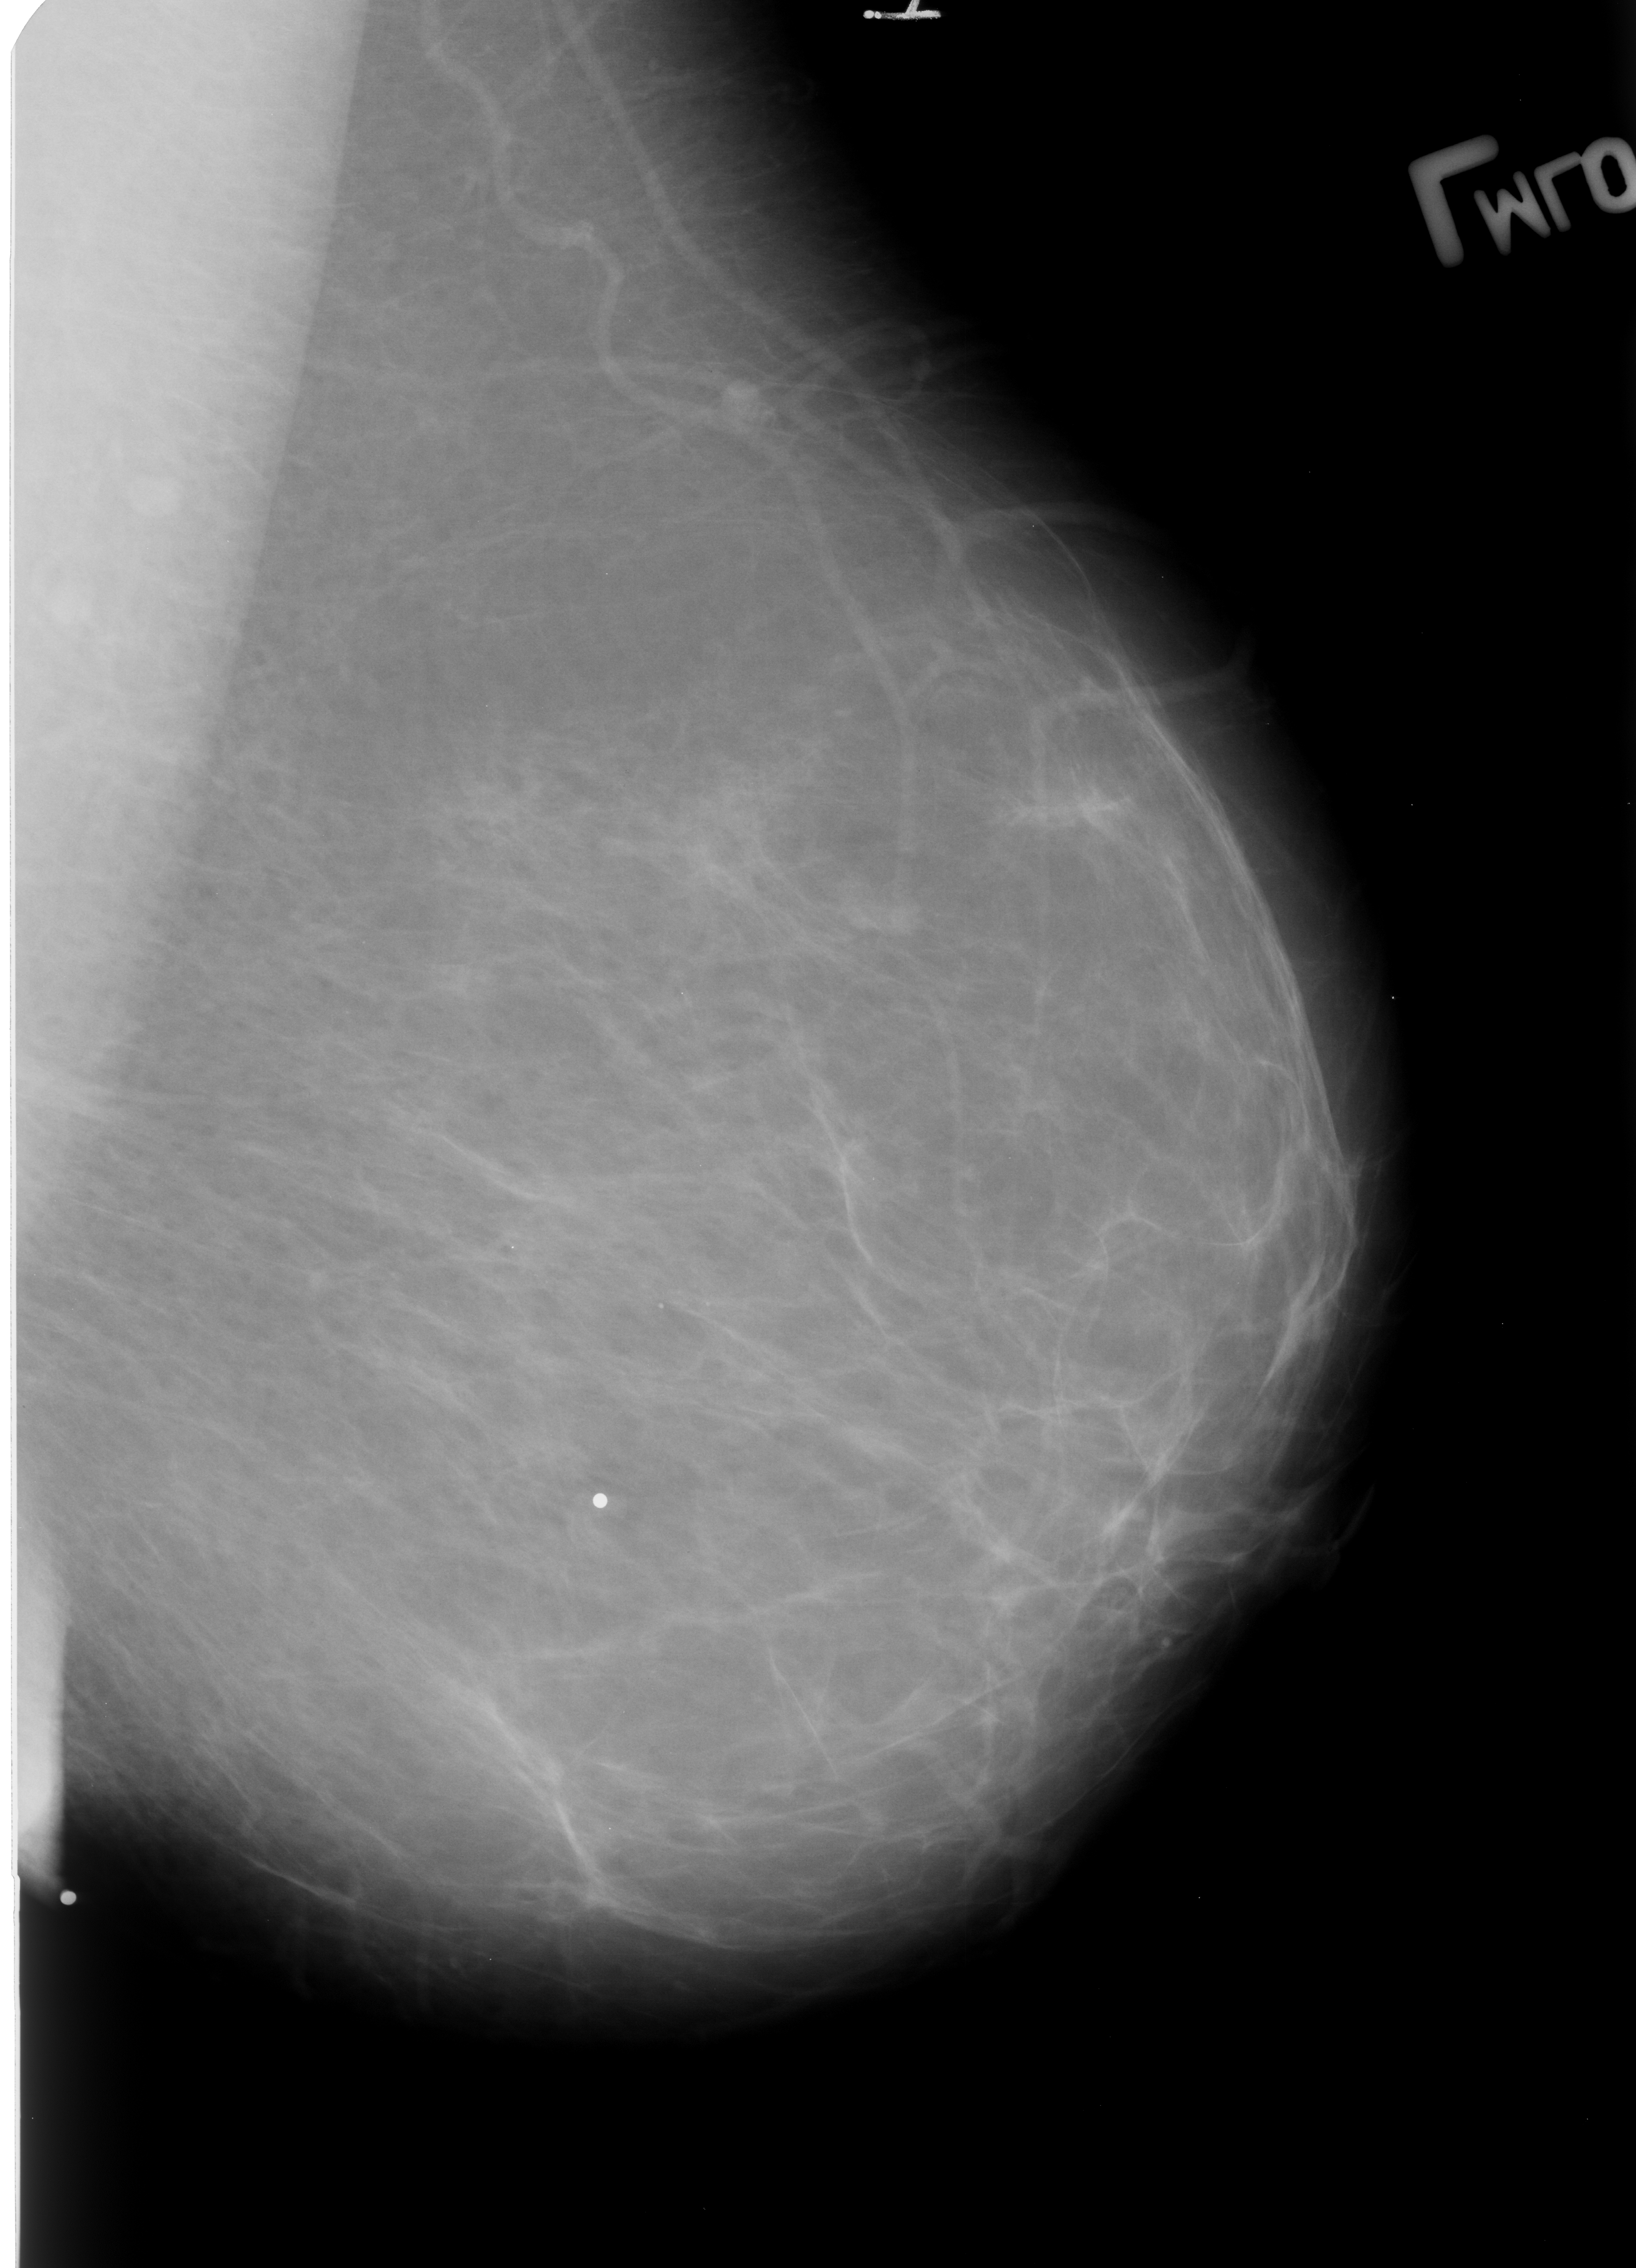
Digitized screen-film mammogram, left breast, mediolateral oblique (MLO) view, BI-RADS breast density category 1 (scale 1–4).
Abnormality record for this image: Finding 1 of 2: mass, shape lymph node, margins circumscribed; BI-RADS assessment category 3; subtlety rating 2 on a 1 (subtle) to 5 (obvious) scale; benign without callback (not worked up further). Finding 2 of 2: mass, shape lymph node, margins circumscribed; BI-RADS assessment category 3; subtlety rating 2 on a 1 (subtle) to 5 (obvious) scale; benign without callback (not worked up further).